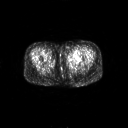
FDG PET of an extremity soft-tissue mass (from a PET/CT study), one axial slice. Slice 13 of 267 in the series (ordered by position). 128 × 128 image matrix, field of view 700 × 700 mm. Female patient, age 47 years. From the clinical record (not read from this slice): histological type: myxofibrosarcoma; grade: intermediate; site of the primary tumour: left thigh.
Annotated regions visible in this slice (expert contour drawn on MRI and transferred to this co-registered scan by the dataset authors):
- gross tumour volume including surrounding oedema: bounding box <67,54,82,62> (left, top, right, bottom; pixels)
- gross tumour volume (mass): <75,54,78,56>